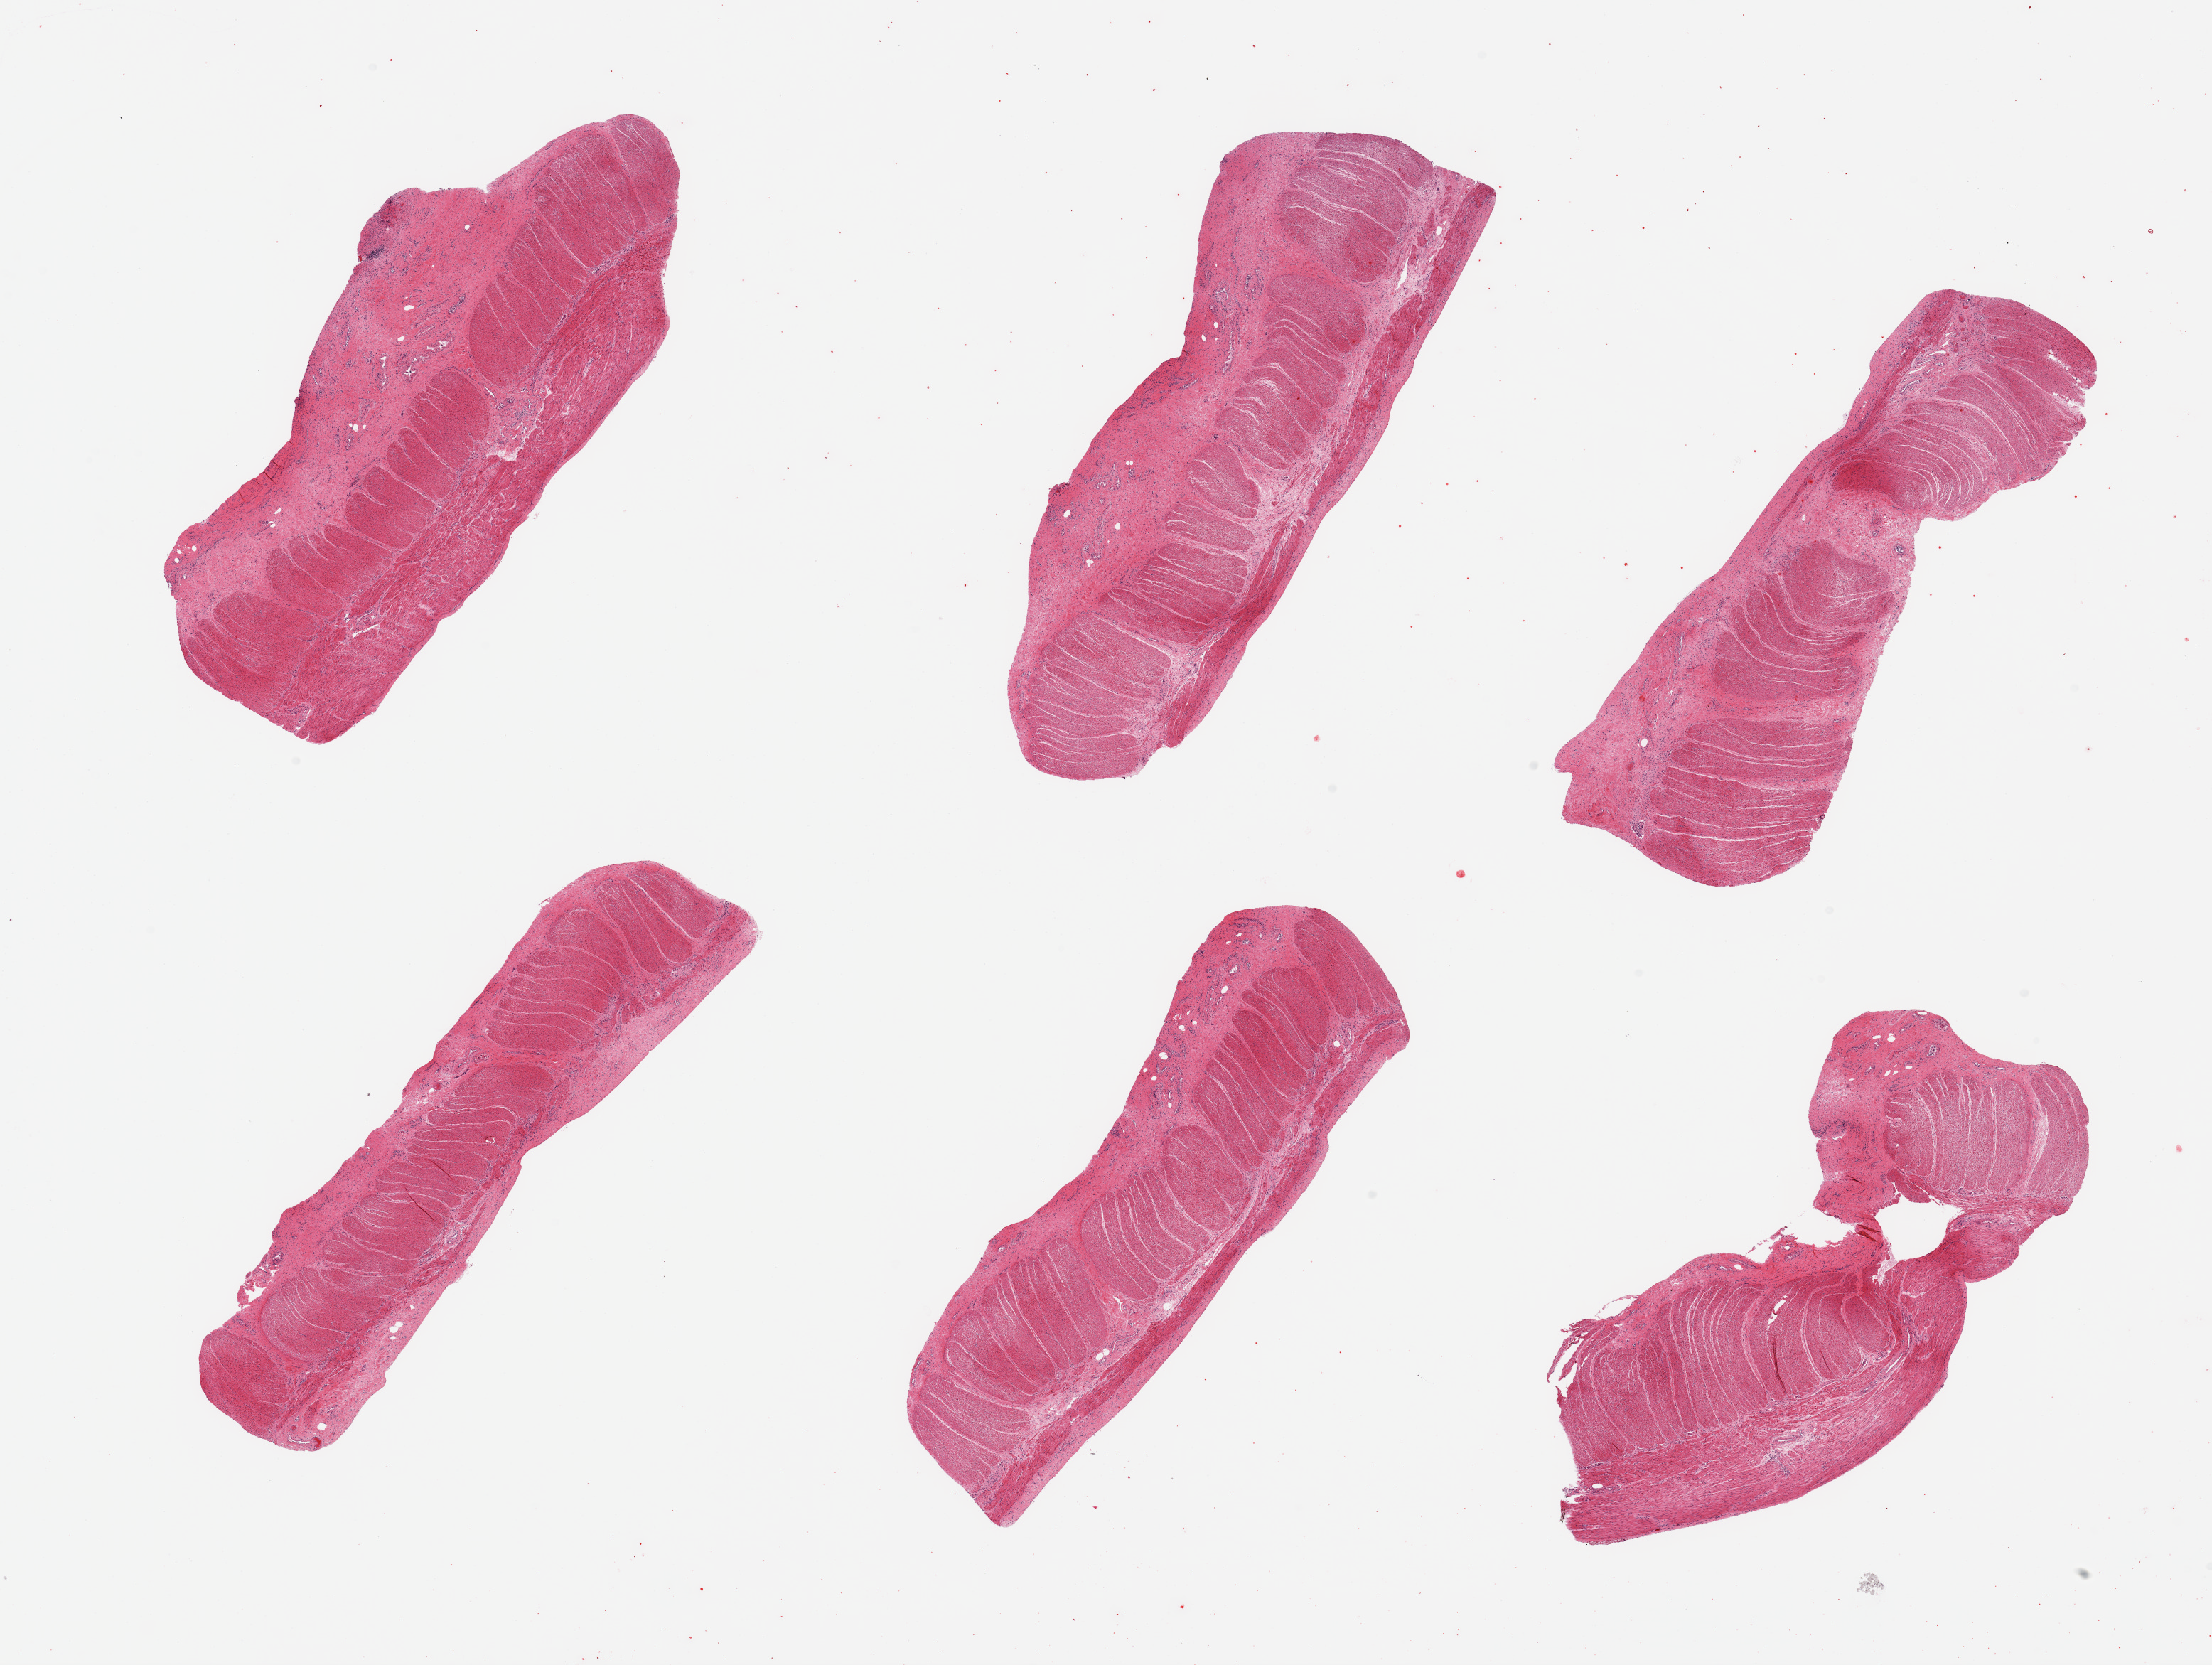
Hematoxylin and eosin (H&E) whole-slide image — whole scanned area (about 24.6 x 18.5 mm) shown as a low-resolution overview, PAXgene-fixed paraffin-embedded (PFPE) section, target tissue: sigmoid colon, tissue donor sample. Female donor.
• pathologist's review note for this sample: 6 pieces; muscle intact; fibrous submucosa is up to 1.2mm thick